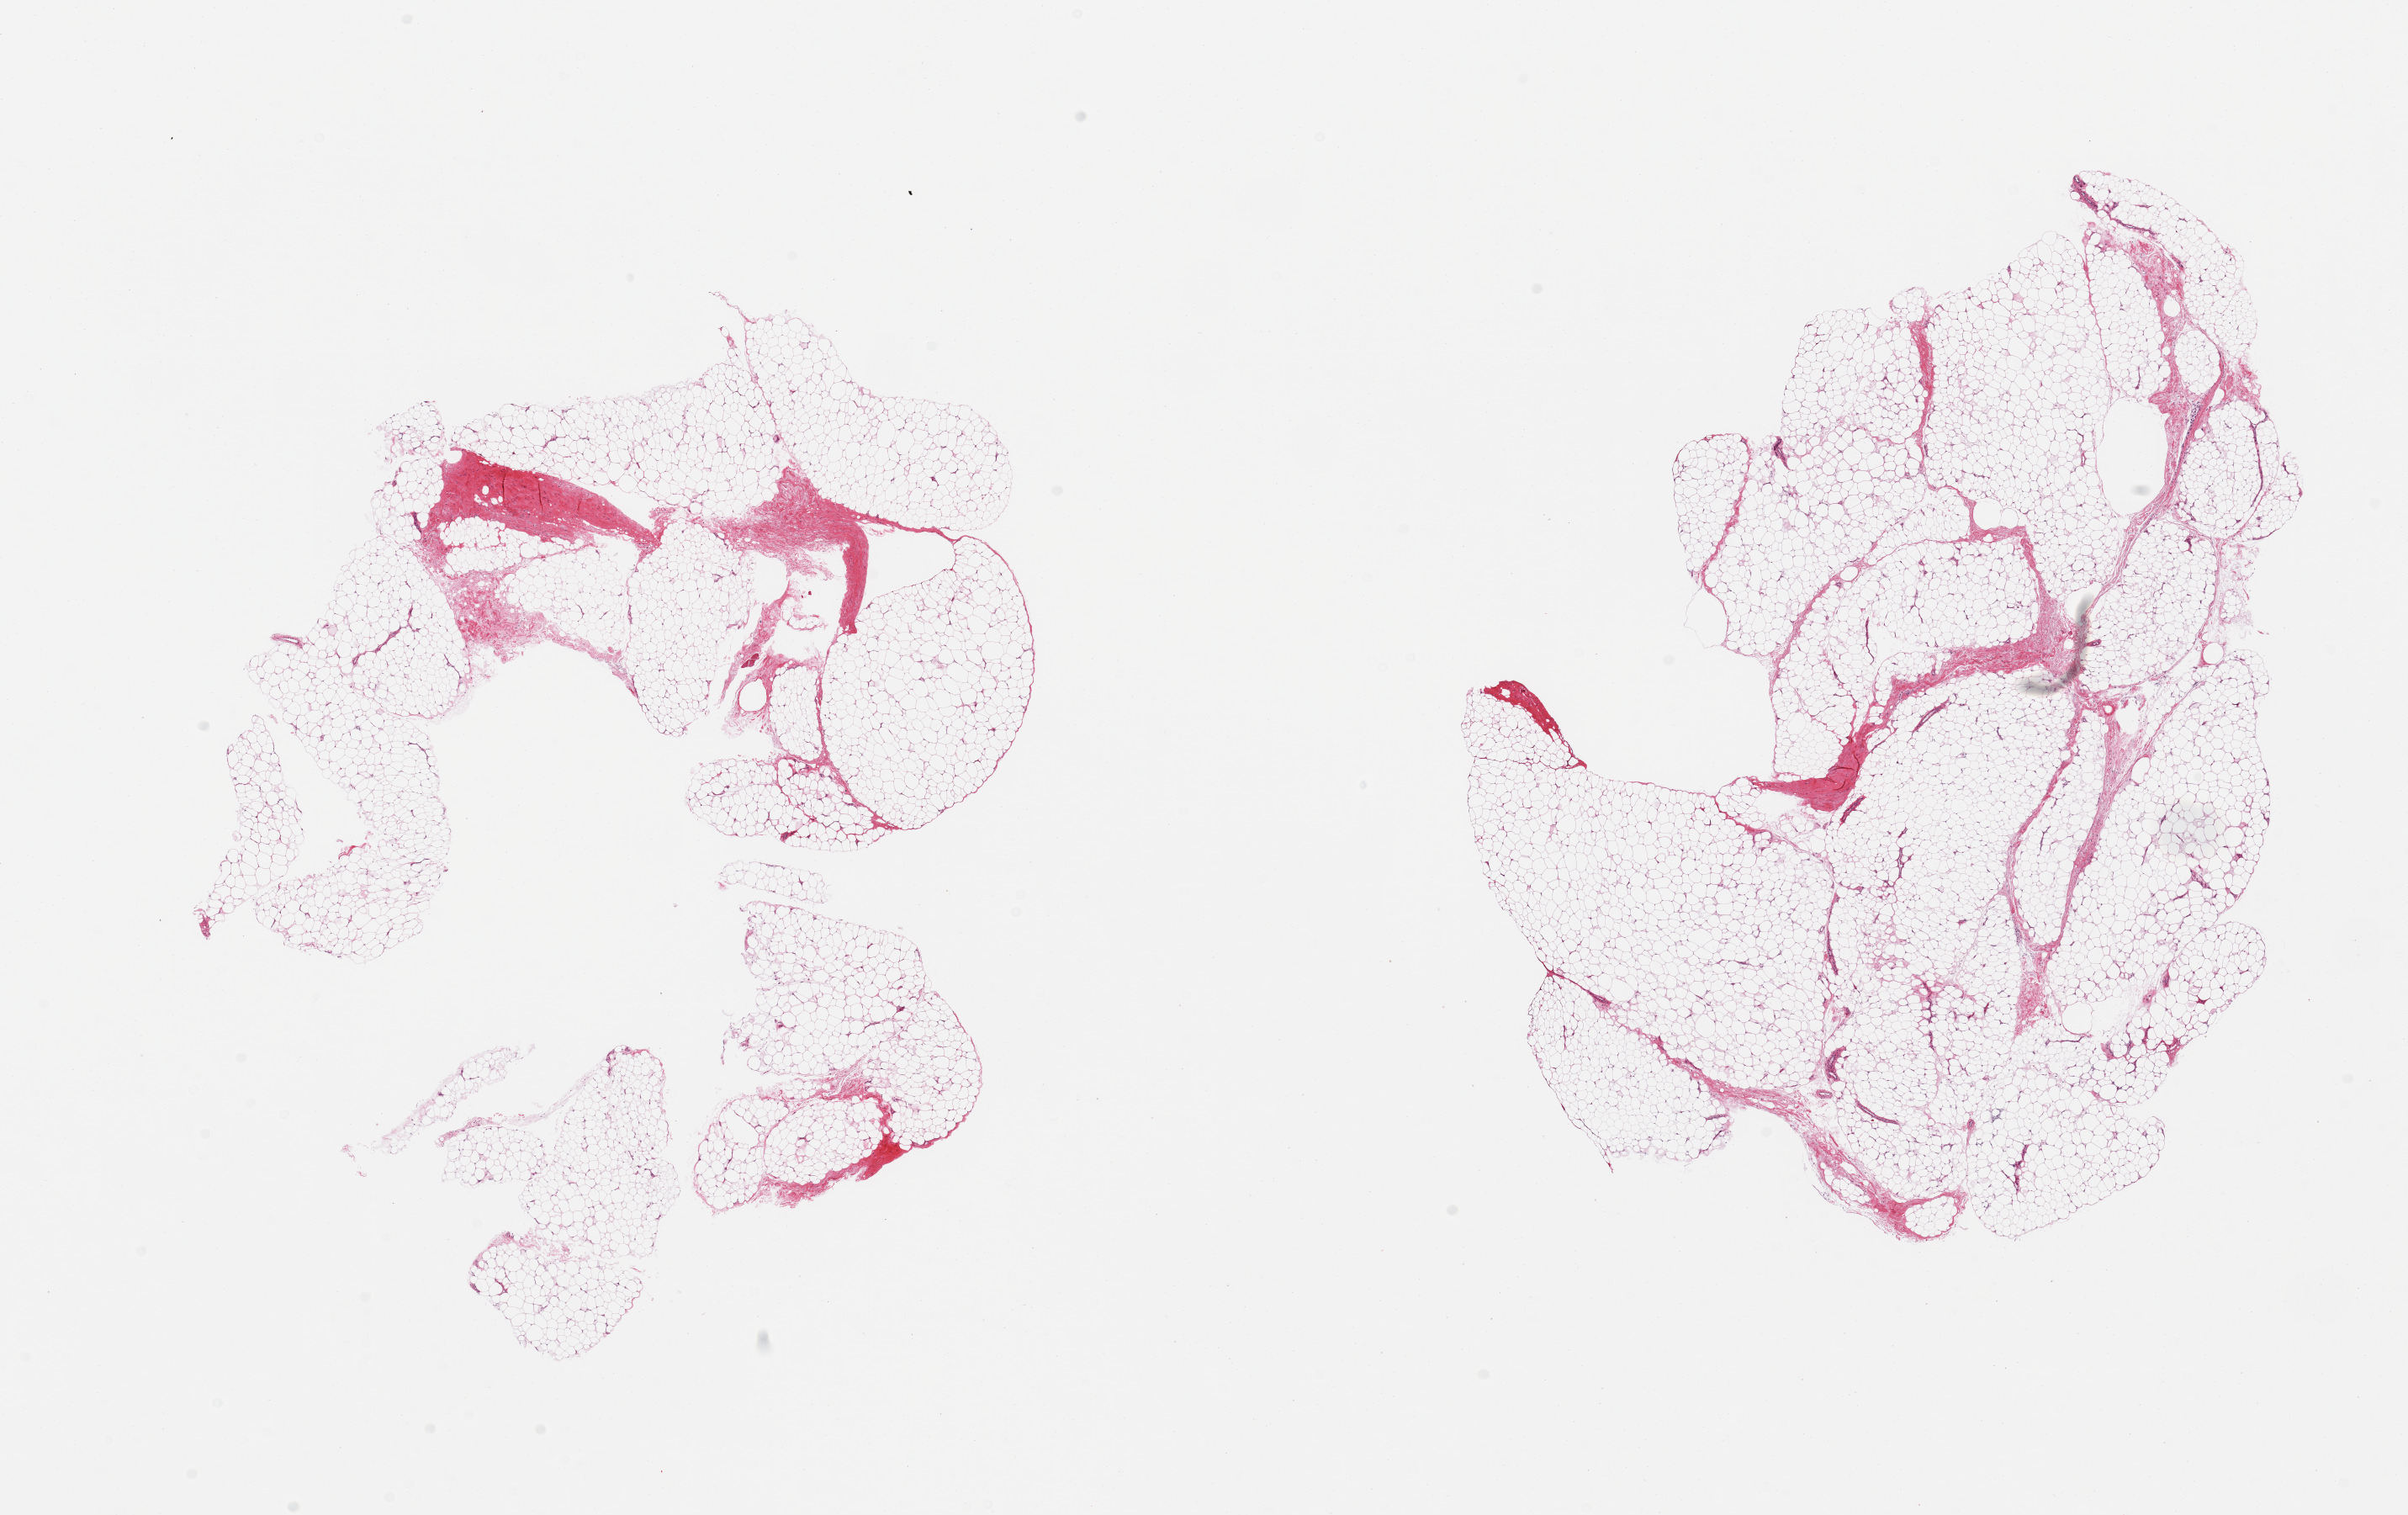
Whole-slide image, hematoxylin and eosin (H&E) stain, shown as a low-resolution overview of the whole scanned area (about 22.6 x 14.2 mm). PAXgene-fixed, paraffin-embedded tissue. Section of adipose tissue (target tissue). Tissue donor sample. Donor: male.
Pathologist's review note for this sample: 2 pieces, ~10% fascia/vascular elements.